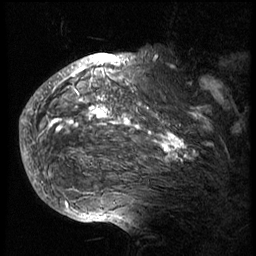
Breast MRI (dynamic contrast-enhanced), one sagittal slice. Slice 55 of 74 in the series (ordered by position). 3 images stored at this slice position (order not interpretable as contrast timing). 1.5 T. TE 4.2 ms, TR 8.9 ms. 256 × 256 image matrix, field of view 200 × 200 mm. Female patient, age 57 years. From the clinical record (not read from this slice): setting: breast cancer imaged before/during neoadjuvant chemotherapy; receptor status: HER2-positive.
Annotated regions visible in this slice (semi-automatically segmented with operator editing):
- analysis volume of interest (the breast-tissue region the enhancement analysis was run in; not a lesion): bounding box [x1, y1, x2, y2] px = [40, 62, 234, 175]
- tumour enhancement mask (voxels above the 140 % enhancement threshold inside the analysis volume of interest): [40, 66, 217, 161]